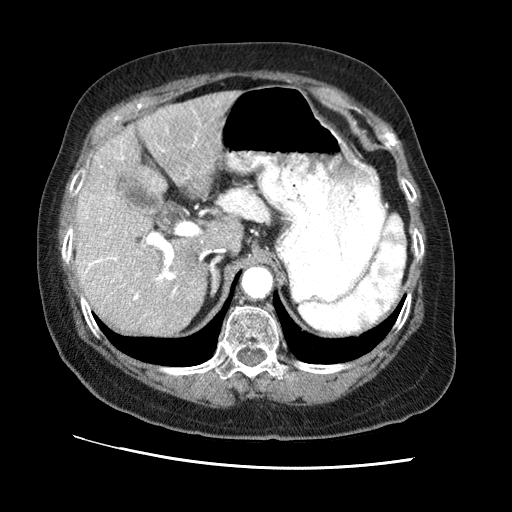
Contrast-enhanced abdominal CT (liver protocol), one axial slice. Slice 41 of 65 in the series (ordered by position). Reconstruction kernel STANDARD. Soft-tissue window (W 400 / L 40 HU). 512 × 512 image matrix. From the clinical record (not read from this slice): diagnosis: hepatocellular carcinoma (patient treated with transarterial chemoembolisation; whether this scan precedes or follows treatment is not stated here); TNM stage (as recorded): Stage-II; Child-Pugh class: A; tumour differentiation: no biopsy; tumour nodularity: multinodular.
Structures marked on this image (semi-automatic segmentation, software-assisted and operator-edited):
- liver parenchyma outside the tumour (the mass and vessels are separate outlines, so this box may not span the whole liver): bounding box <75,90,241,334> (left, top, right, bottom; pixels)
- liver vessels: <84,112,204,300>